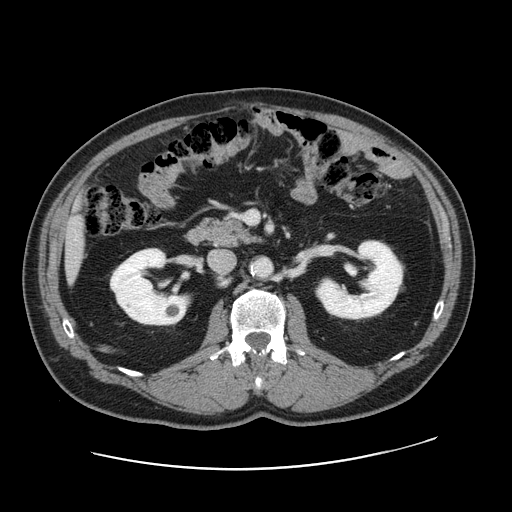
Contrast-enhanced abdominal CT, one axial slice; slice 67 of 178 in the series (ordered by position); 120 kVp; intravenous contrast given; soft-tissue window (W 400 / L 40 HU); 2.5 mm slice thickness; 512 × 512 image matrix, field of view 403 × 403 mm. Male patient, age 63 years. From the clinical record (not read from this slice): diagnosis: colorectal cancer liver metastases, imaged before liver resection; multiple liver metastases: yes; largest metastasis: 8 cm; disease in both lobes: yes.
Structures marked on this image (expert manual segmentation):
- liver: box from (x=67, y=218) to (x=85, y=274) px